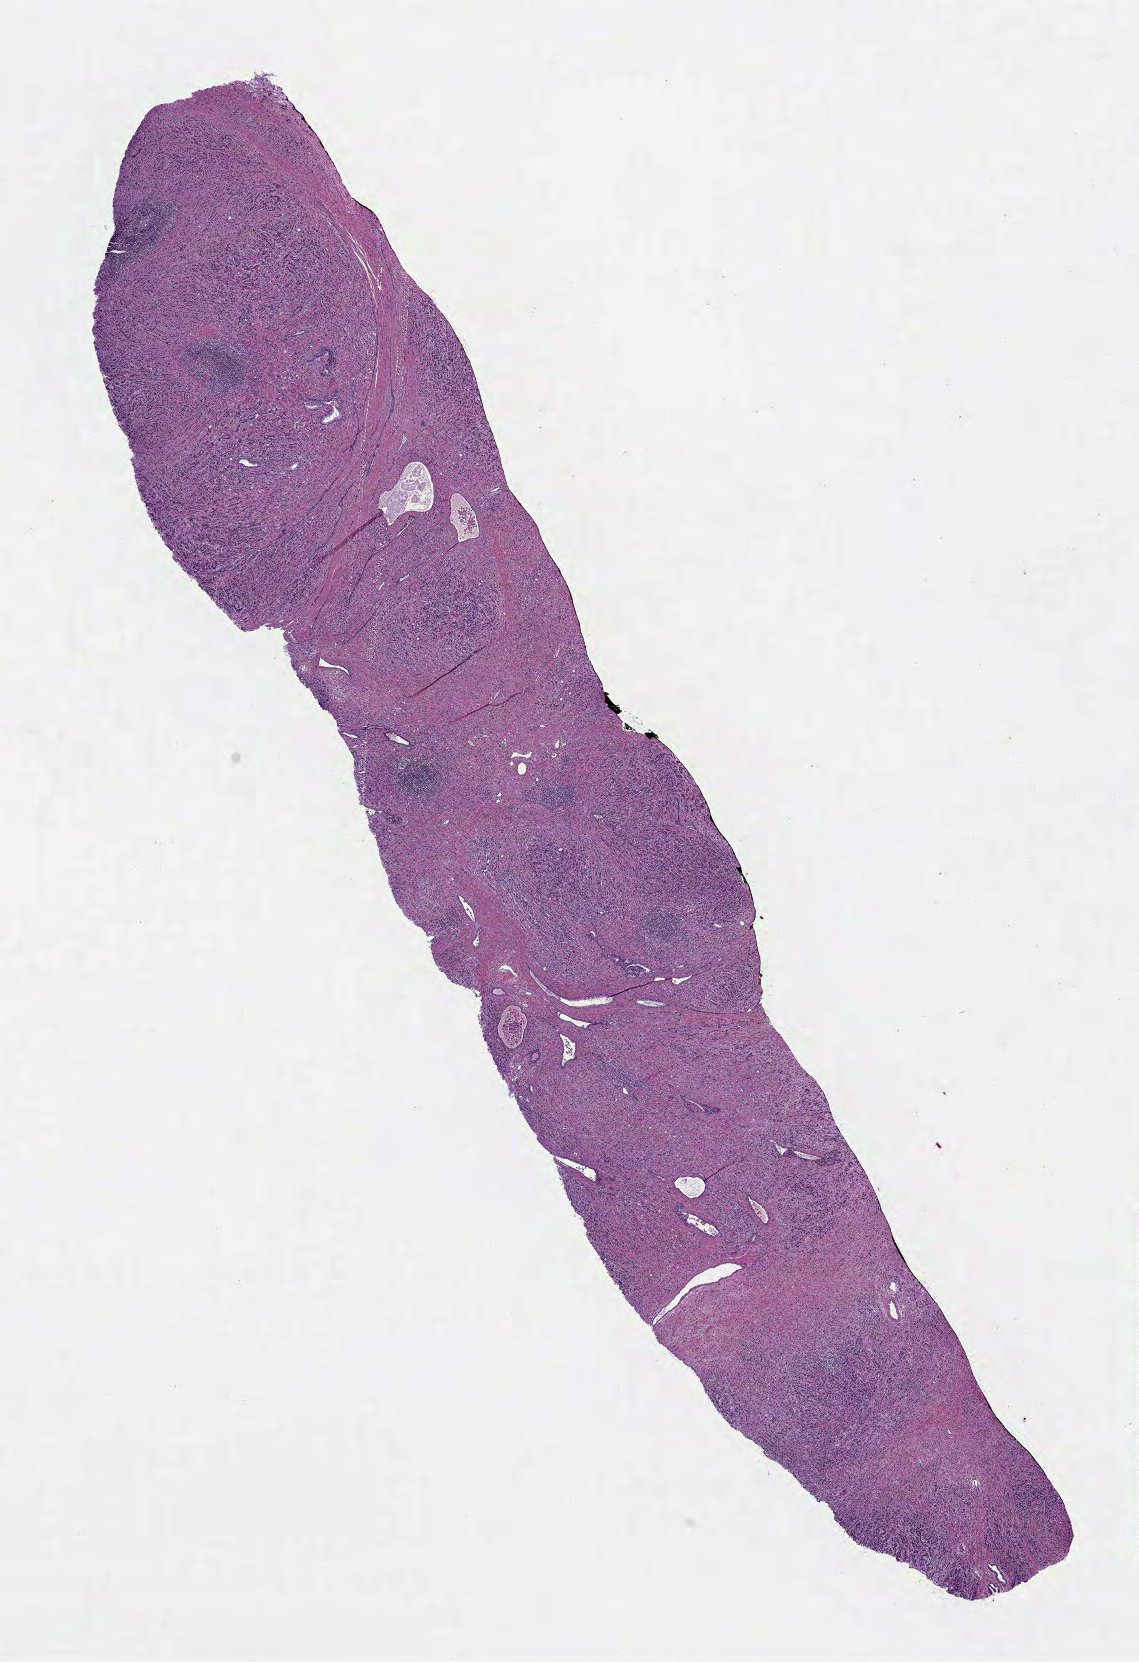
H&E whole-slide image — low-resolution overview of the scanned area, about 9.2 x 13.4 mm, formalin-fixed paraffin-embedded (FFPE) diagnostic section, primary tumour sample from the prostate. Male patient; age at initial diagnosis 68 years. Gleason score: 9 (4+5).
- histologic diagnosis: Adenocarcinoma, NOS
- lymph nodes positive (case pathology): 0 of 5 examined